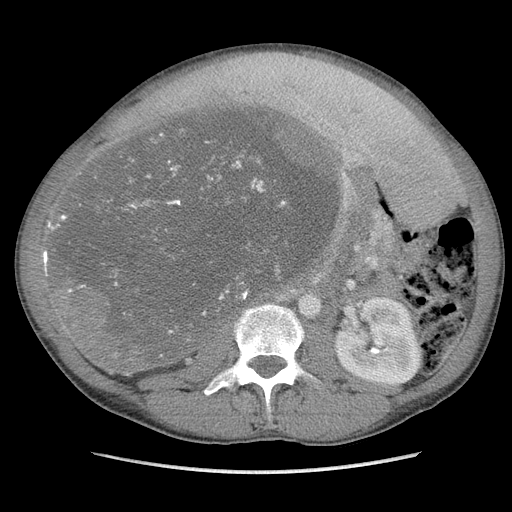
Contrast-enhanced abdominal CT, one axial slice; position 56 of 115 along the scan axis; soft-tissue window (W 400 / L 40 HU); 5 mm slice thickness; 512 × 512 image matrix. Male patient. Case-level facts recorded for this patient, not image findings: diagnosis: adrenocortical carcinoma; tumour side: right adrenal; Ki-67 index: 13 %; stage (as recorded): 3.
Outlined on this slice (semi-automatically segmented with operator editing):
- mass: box from (x=57, y=110) to (x=331, y=374) px